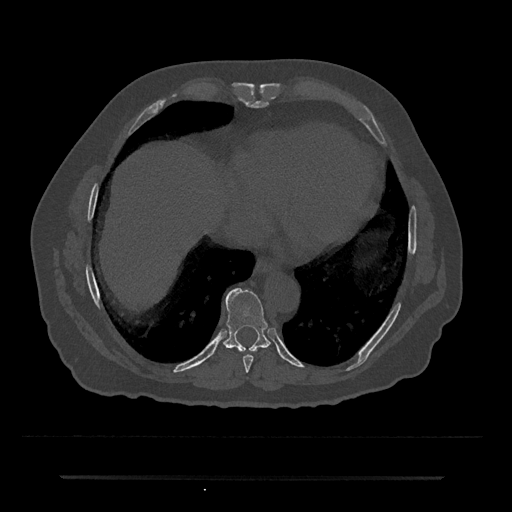
CT including the spine, one axial slice. Slice 294 of 797 in the series (ordered by position). 120 kVp. Bone window (W 1800 / L 400 HU). 0.5 mm slice thickness. 512 × 512 image matrix. Patient: male, 69 years. Case-level facts recorded for this patient, not image findings: primary cancer: prostate.
Annotated regions visible in this slice (semi-automatic segmentation, software-assisted and operator-edited):
- T8 vertebra: bounding box [x1, y1, x2, y2] px = [243, 355, 253, 372]
- T9 vertebra: [223, 288, 271, 352]